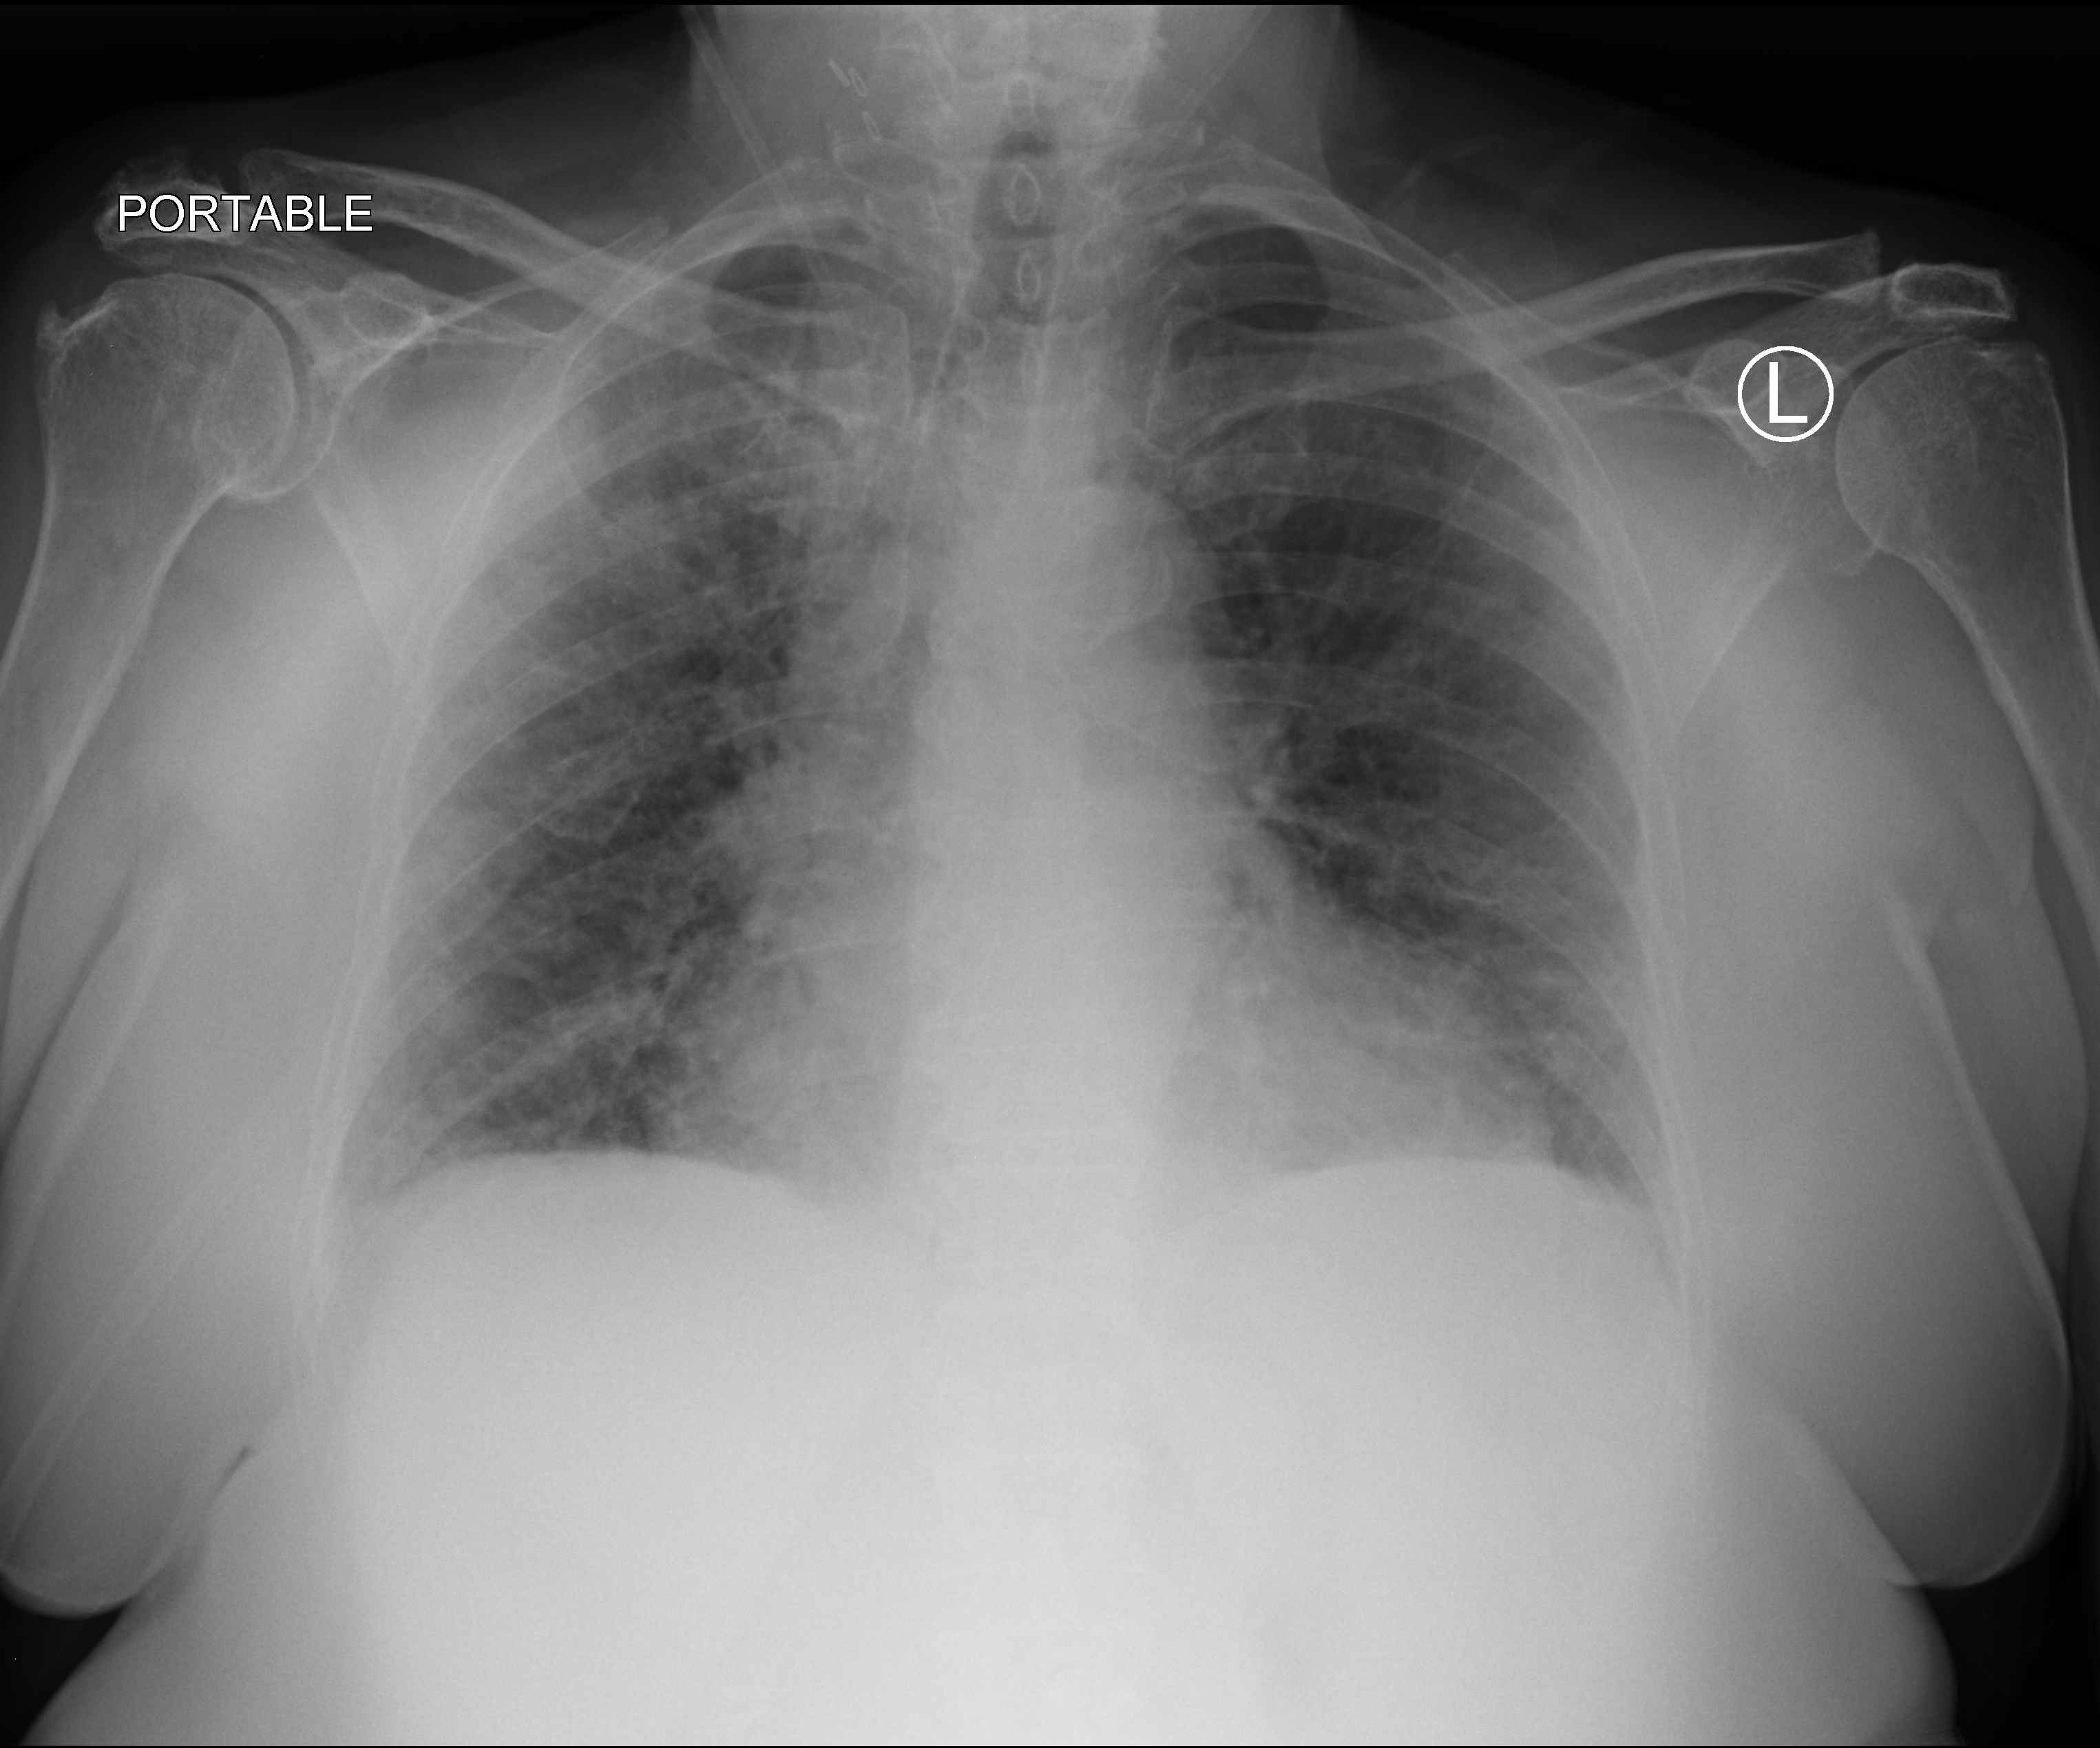
Chest X-ray (portable). Patient hospitalised with COVID-19; female, aged 75–90 years.
Admission-level facts for this patient (not findings on this image; timing relative to this image not recorded):
- admitted to intensive care during this hospital stay: no
- mechanically ventilated during this hospital stay: no